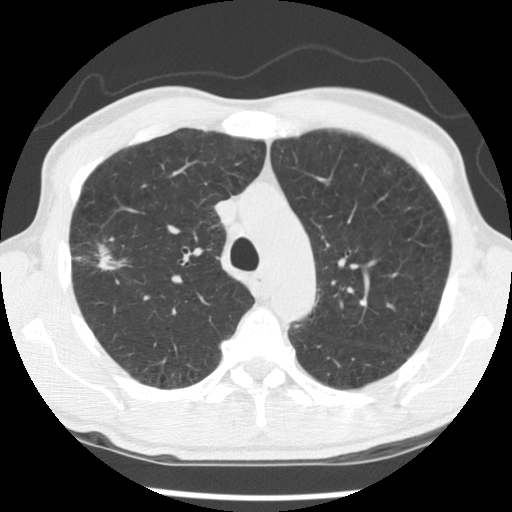
Low-dose screening chest CT, one axial slice. Slice 94 of 138 in the series (ordered by position). 140 kVp. Lung window (W 1500 / L -600 HU). 2.5 mm slice thickness. 512 × 512 image matrix, field of view 320 × 320 mm.
Annotated regions visible in this slice (expert manual segmentation):
- lesion 1 (tumor, upper lobe of right lung): box from (x=96, y=244) to (x=126, y=270) px